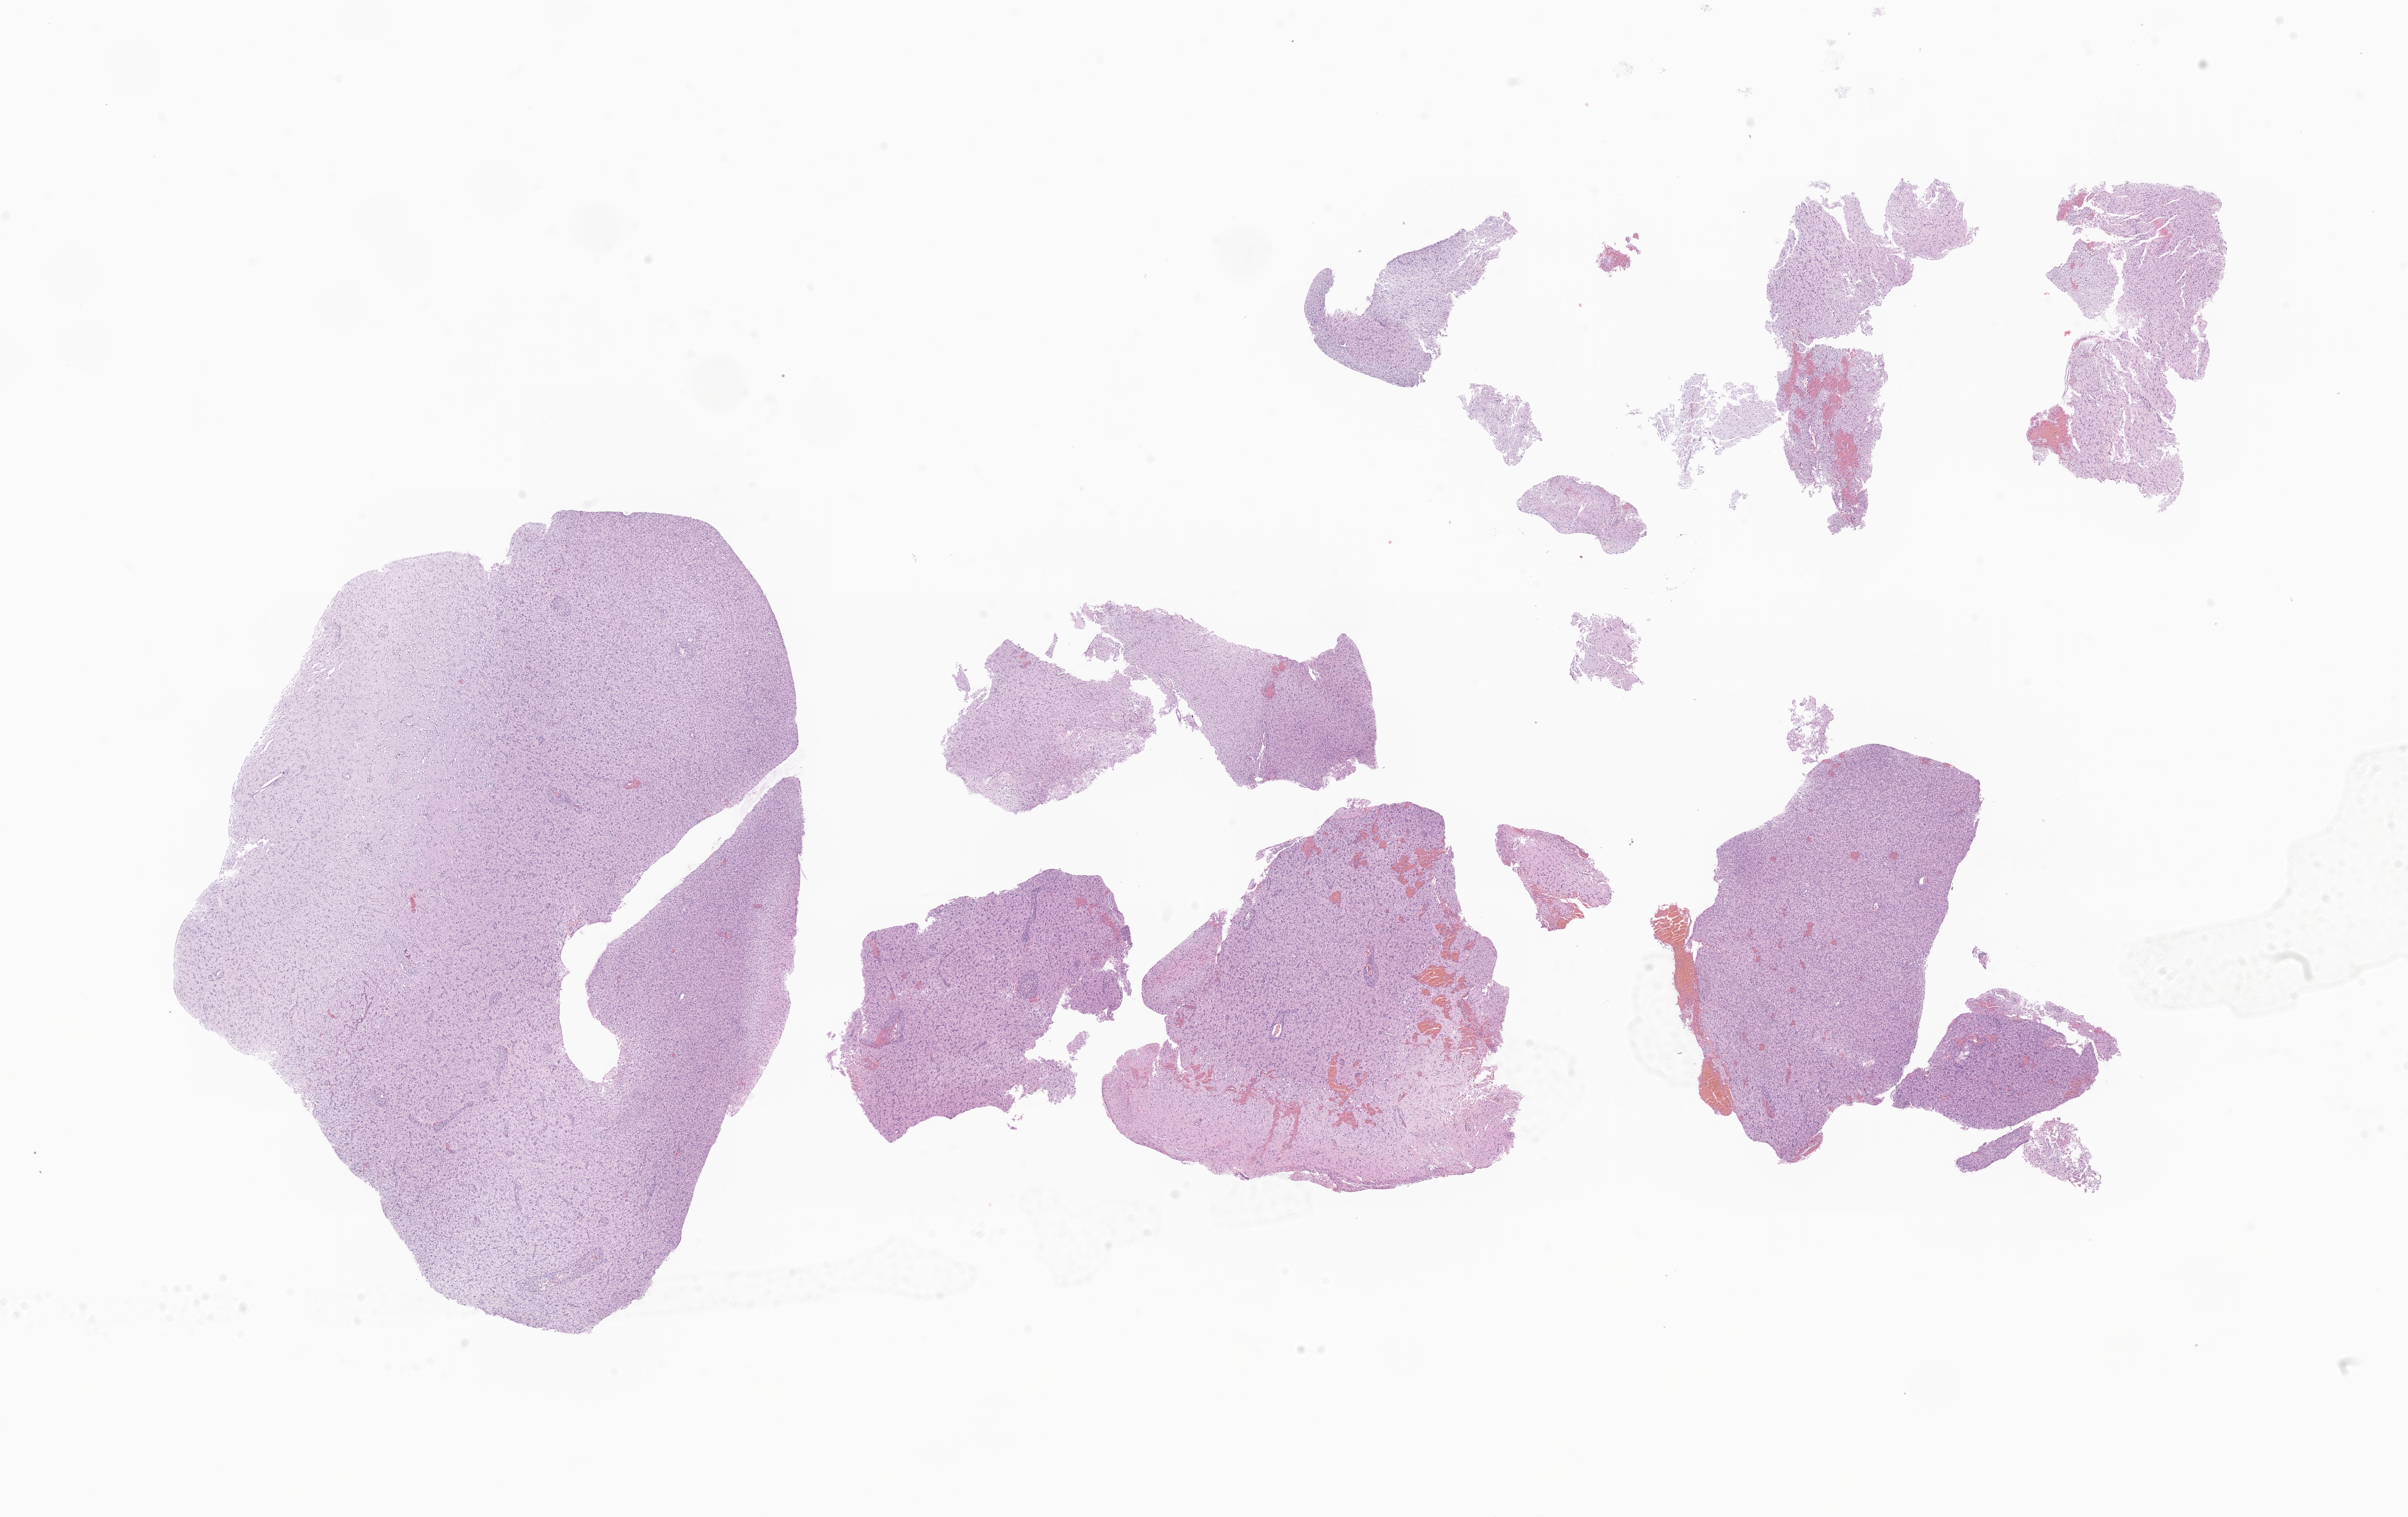
Digitized hematoxylin and eosin (H&E)-stained section of tumor tissue from the brain — shown as a low-resolution overview of the whole scanned area (about 24.9 x 15.7 mm); formalin-fixed paraffin-embedded section. Male patient, age 205 months (17 years 1 month).
* recorded diagnosis: Neoplasm, uncertain whether benign or malignant